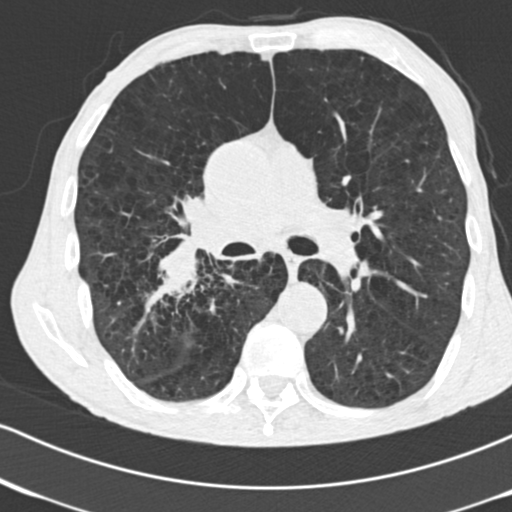
Chest CT (low-dose screening protocol), one axial image, second annual screen, lung window (W 1500 / L -600 HU), 2 mm slice thickness, standard (soft-tissue) reconstruction kernel (B30f), slice 84 of 182 in the series. Male, age 64 years at enrolment. Current smoker at enrolment.
Expert reader's lesion annotation, bounding box (x1, y1, x2, y2) in pixels: (133, 231, 238, 326). Reader record for this screening exam (exam-level; its link to the box is not recorded): non-calcified nodule or mass ≥4 mm, 52 × 37 mm, spiculated (stellate) margins, soft tissue attenuation, pre-existing on the prior screen: no. Lung cancer was diagnosed 28 days after this screen: adenocarcinoma, NOS, right lower lobe, stage IV (AJCC 6th edition), 60 mm at pathology.